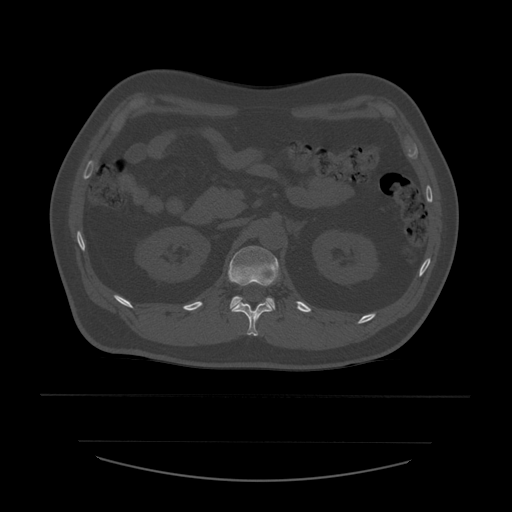
CT including the spine, one axial slice. Position 239 of 532 along the scan axis. Reconstruction kernel STANDARD. 120 kVp. Bone window (W 1800 / L 400 HU). 1.25 mm slice thickness. 512 × 512 image matrix, field of view 441 × 441 mm. Patient age 44 years. From the clinical record (not read from this slice): primary cancer: soft tissue sarcoma.
Structures marked on this image (semi-automatic segmentation, software-assisted and operator-edited):
- L1 vertebra: box from (x=228, y=246) to (x=280, y=311) px
- T12 vertebra: (x=232, y=301)–(x=273, y=336)